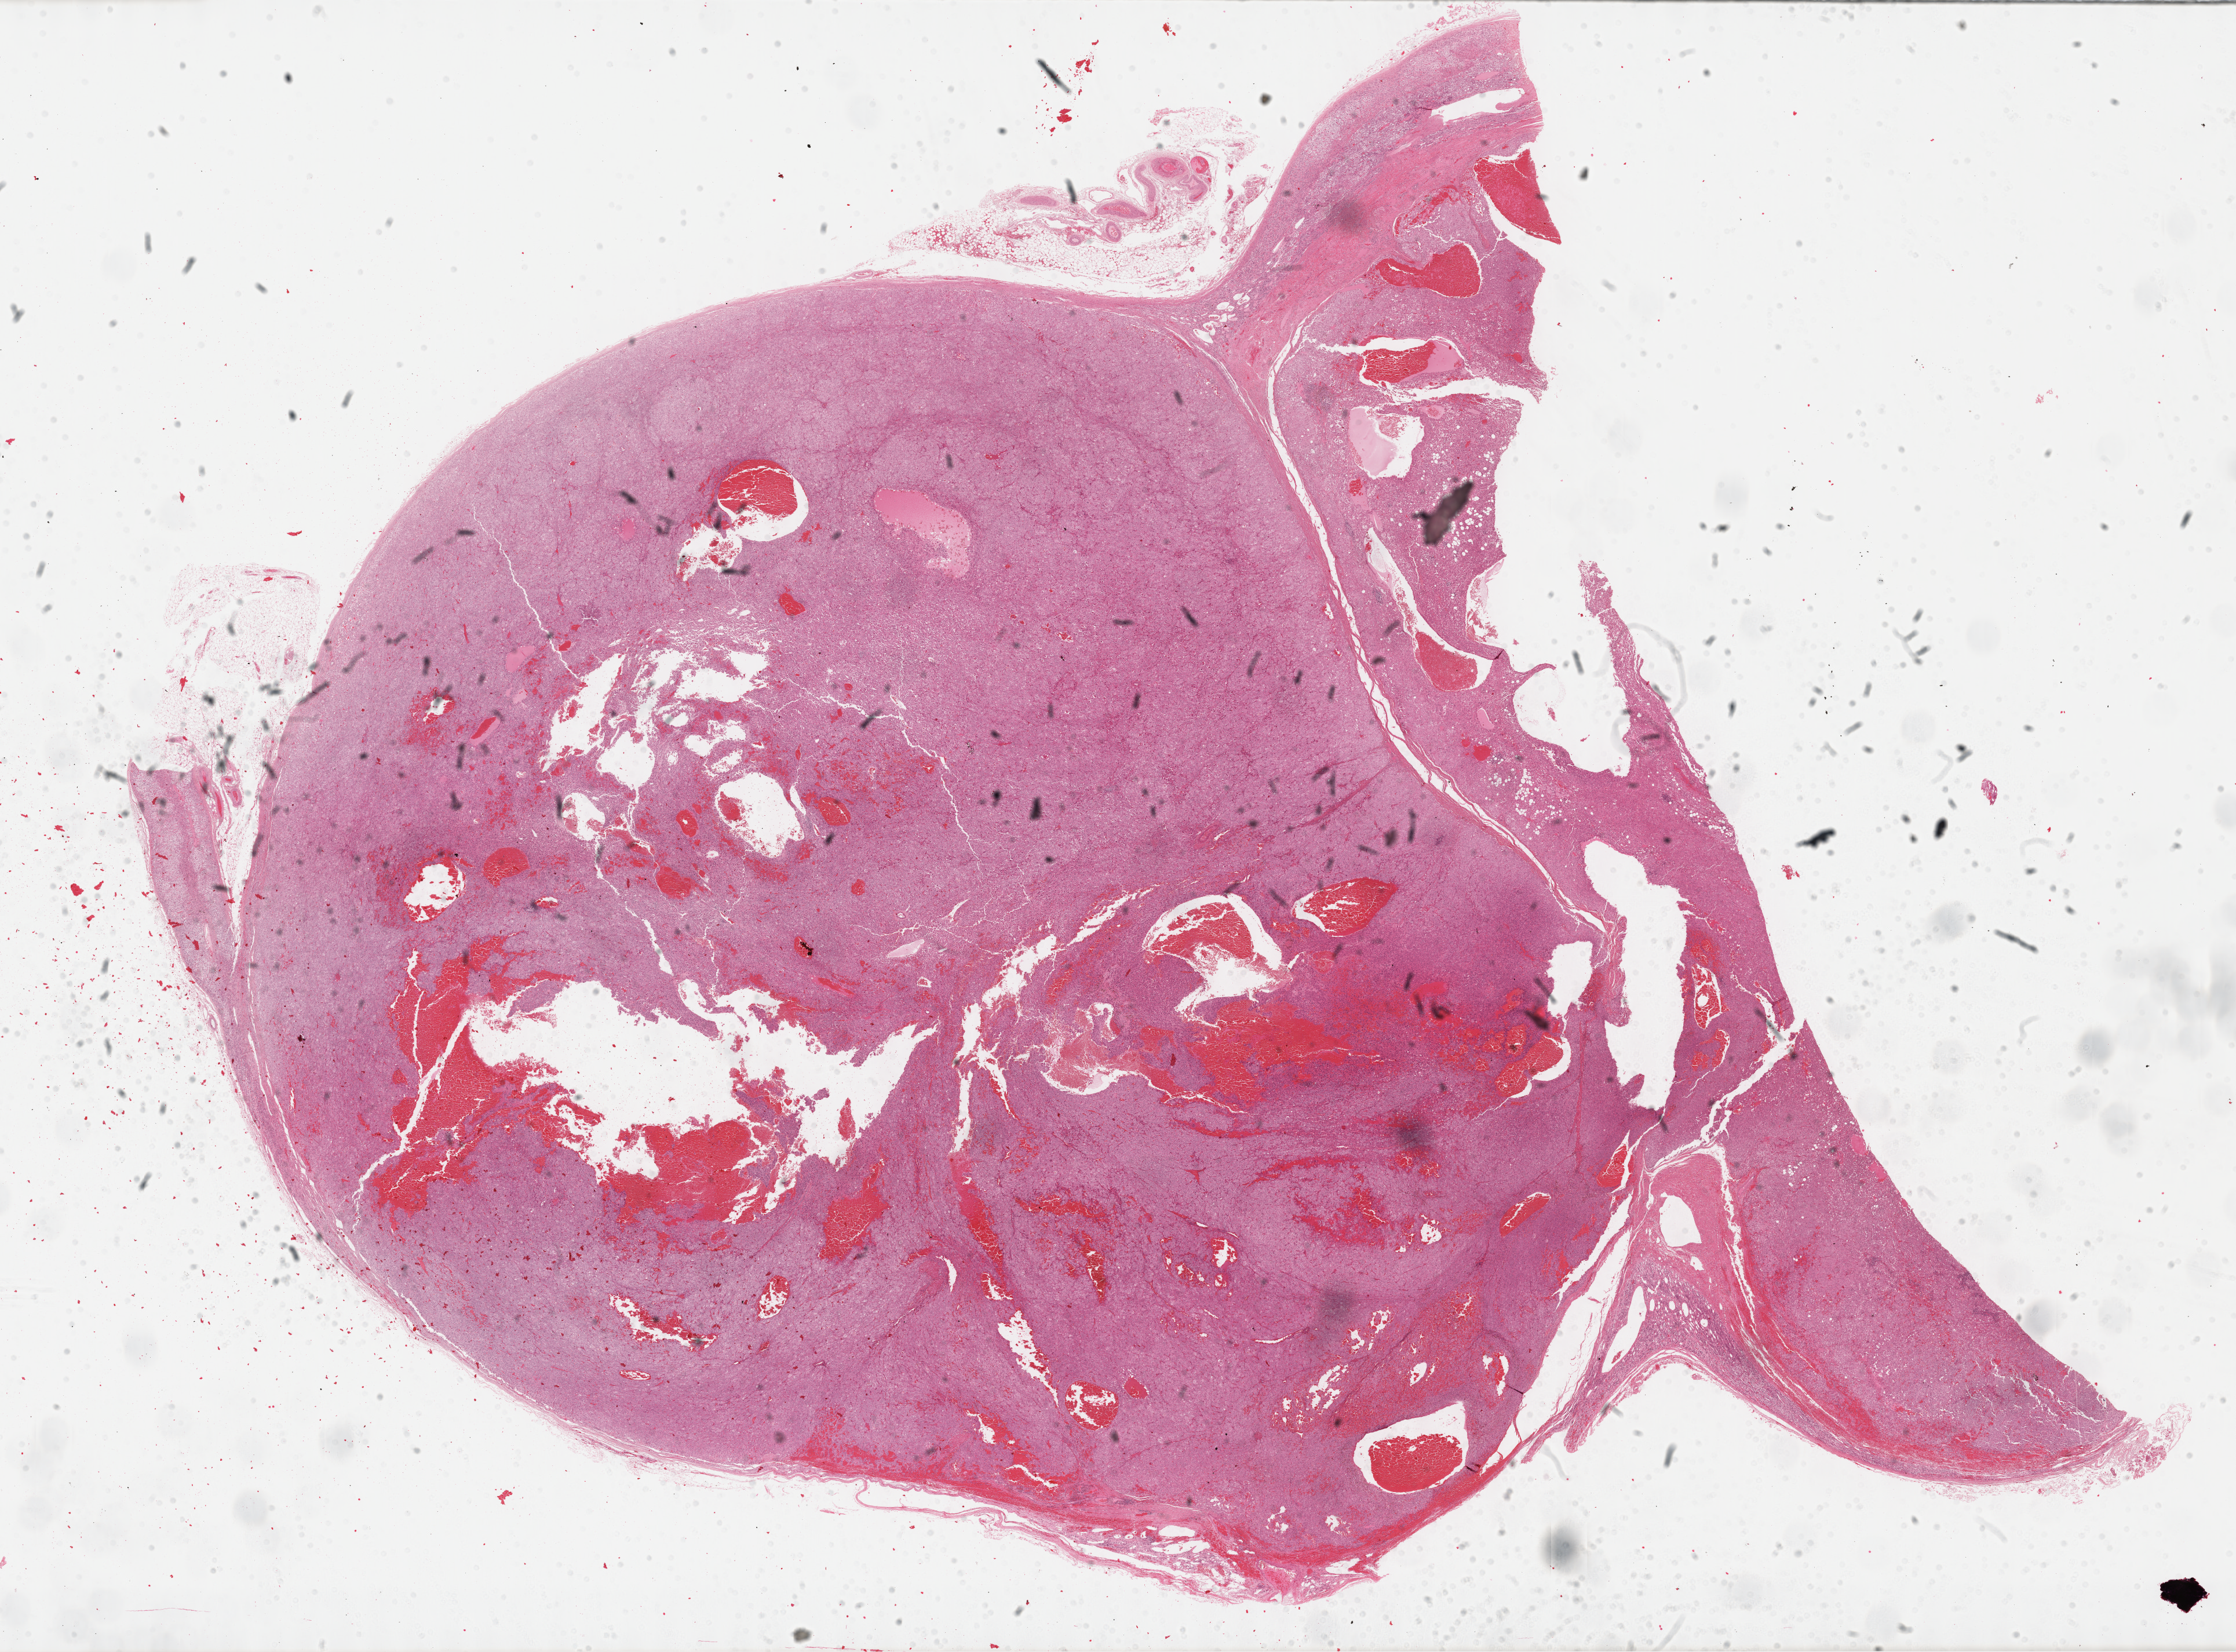
Digitized H&E-stained tissue section (whole slide), shown as a low-resolution overview of the whole scanned area (about 31.2 x 23.1 mm, from a 40x scan); FFPE section; adrenal cortex, primary tumour sample. Male patient; age at initial diagnosis 22 years.
• histologic diagnosis: Adrenal cortical carcinoma (cortex of adrenal gland)